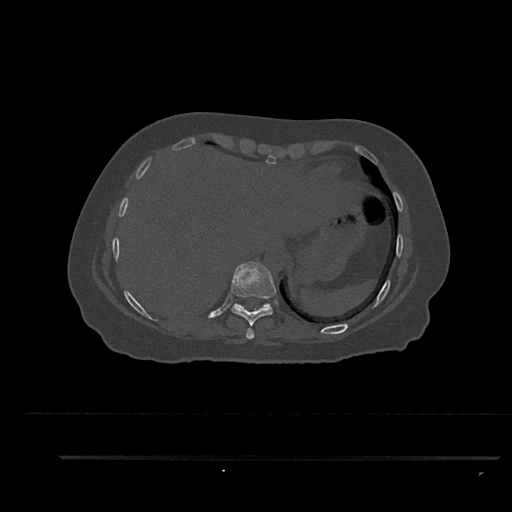
CT including the spine, one axial slice. Position 404 of 797 along the scan axis. Reconstruction kernel Br40s/3. 120 kVp. Bone window (W 1800 / L 400 HU). 0.5 mm slice thickness. 512 × 512 image matrix, field of view 408 × 408 mm. Female patient, age 44 years. From the clinical record (not read from this slice): primary cancer: renal.
Structures marked on this image (semi-automatic segmentation, software-assisted and operator-edited):
- T10 vertebra: box from (x=234, y=303) to (x=272, y=308) px
- T8 vertebra: (x=246, y=328)–(x=254, y=339)
- T9 vertebra: (x=231, y=261)–(x=276, y=326)